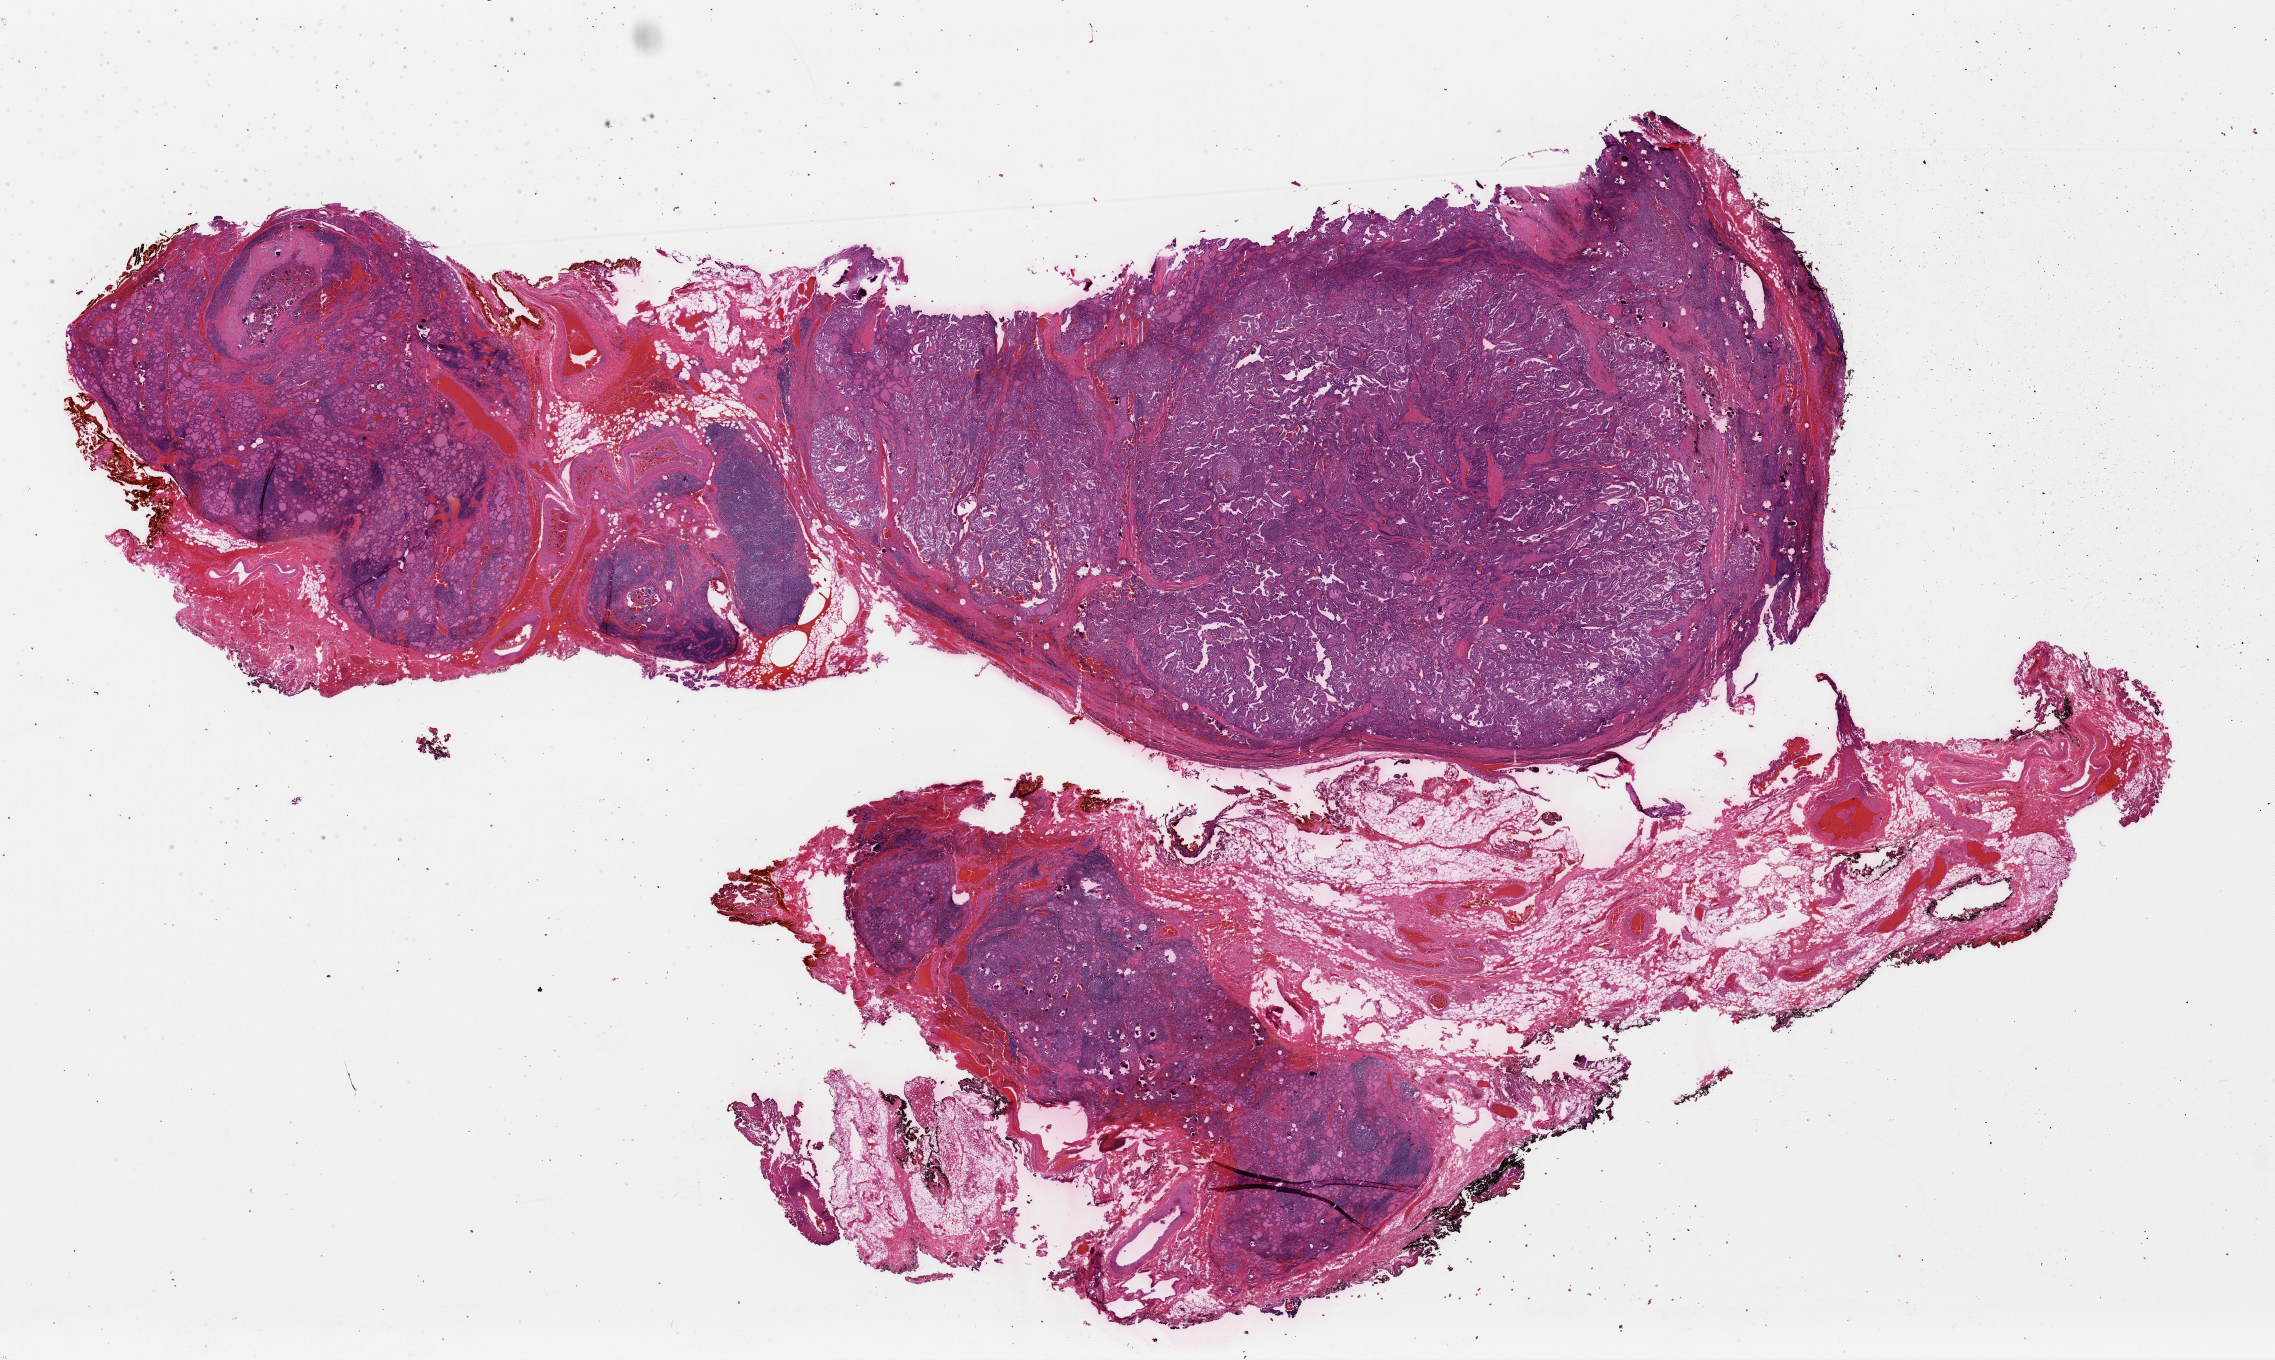
Digitized Hematoxylin and eosin (H&E) stained tissue section (whole slide), shown as a low-resolution overview of the whole scanned area (about 35.9 x 21.5 mm). FFPE section. Thyroid, primary tumour sample. Patient: female, age at initial diagnosis 26 years.
Pathologic diagnosis: Papillary adenocarcinoma, NOS. Lymph nodes positive (case pathology): 3 of 15 examined. Laterality: midline. AJCC pathologic stage: I (7th edition).